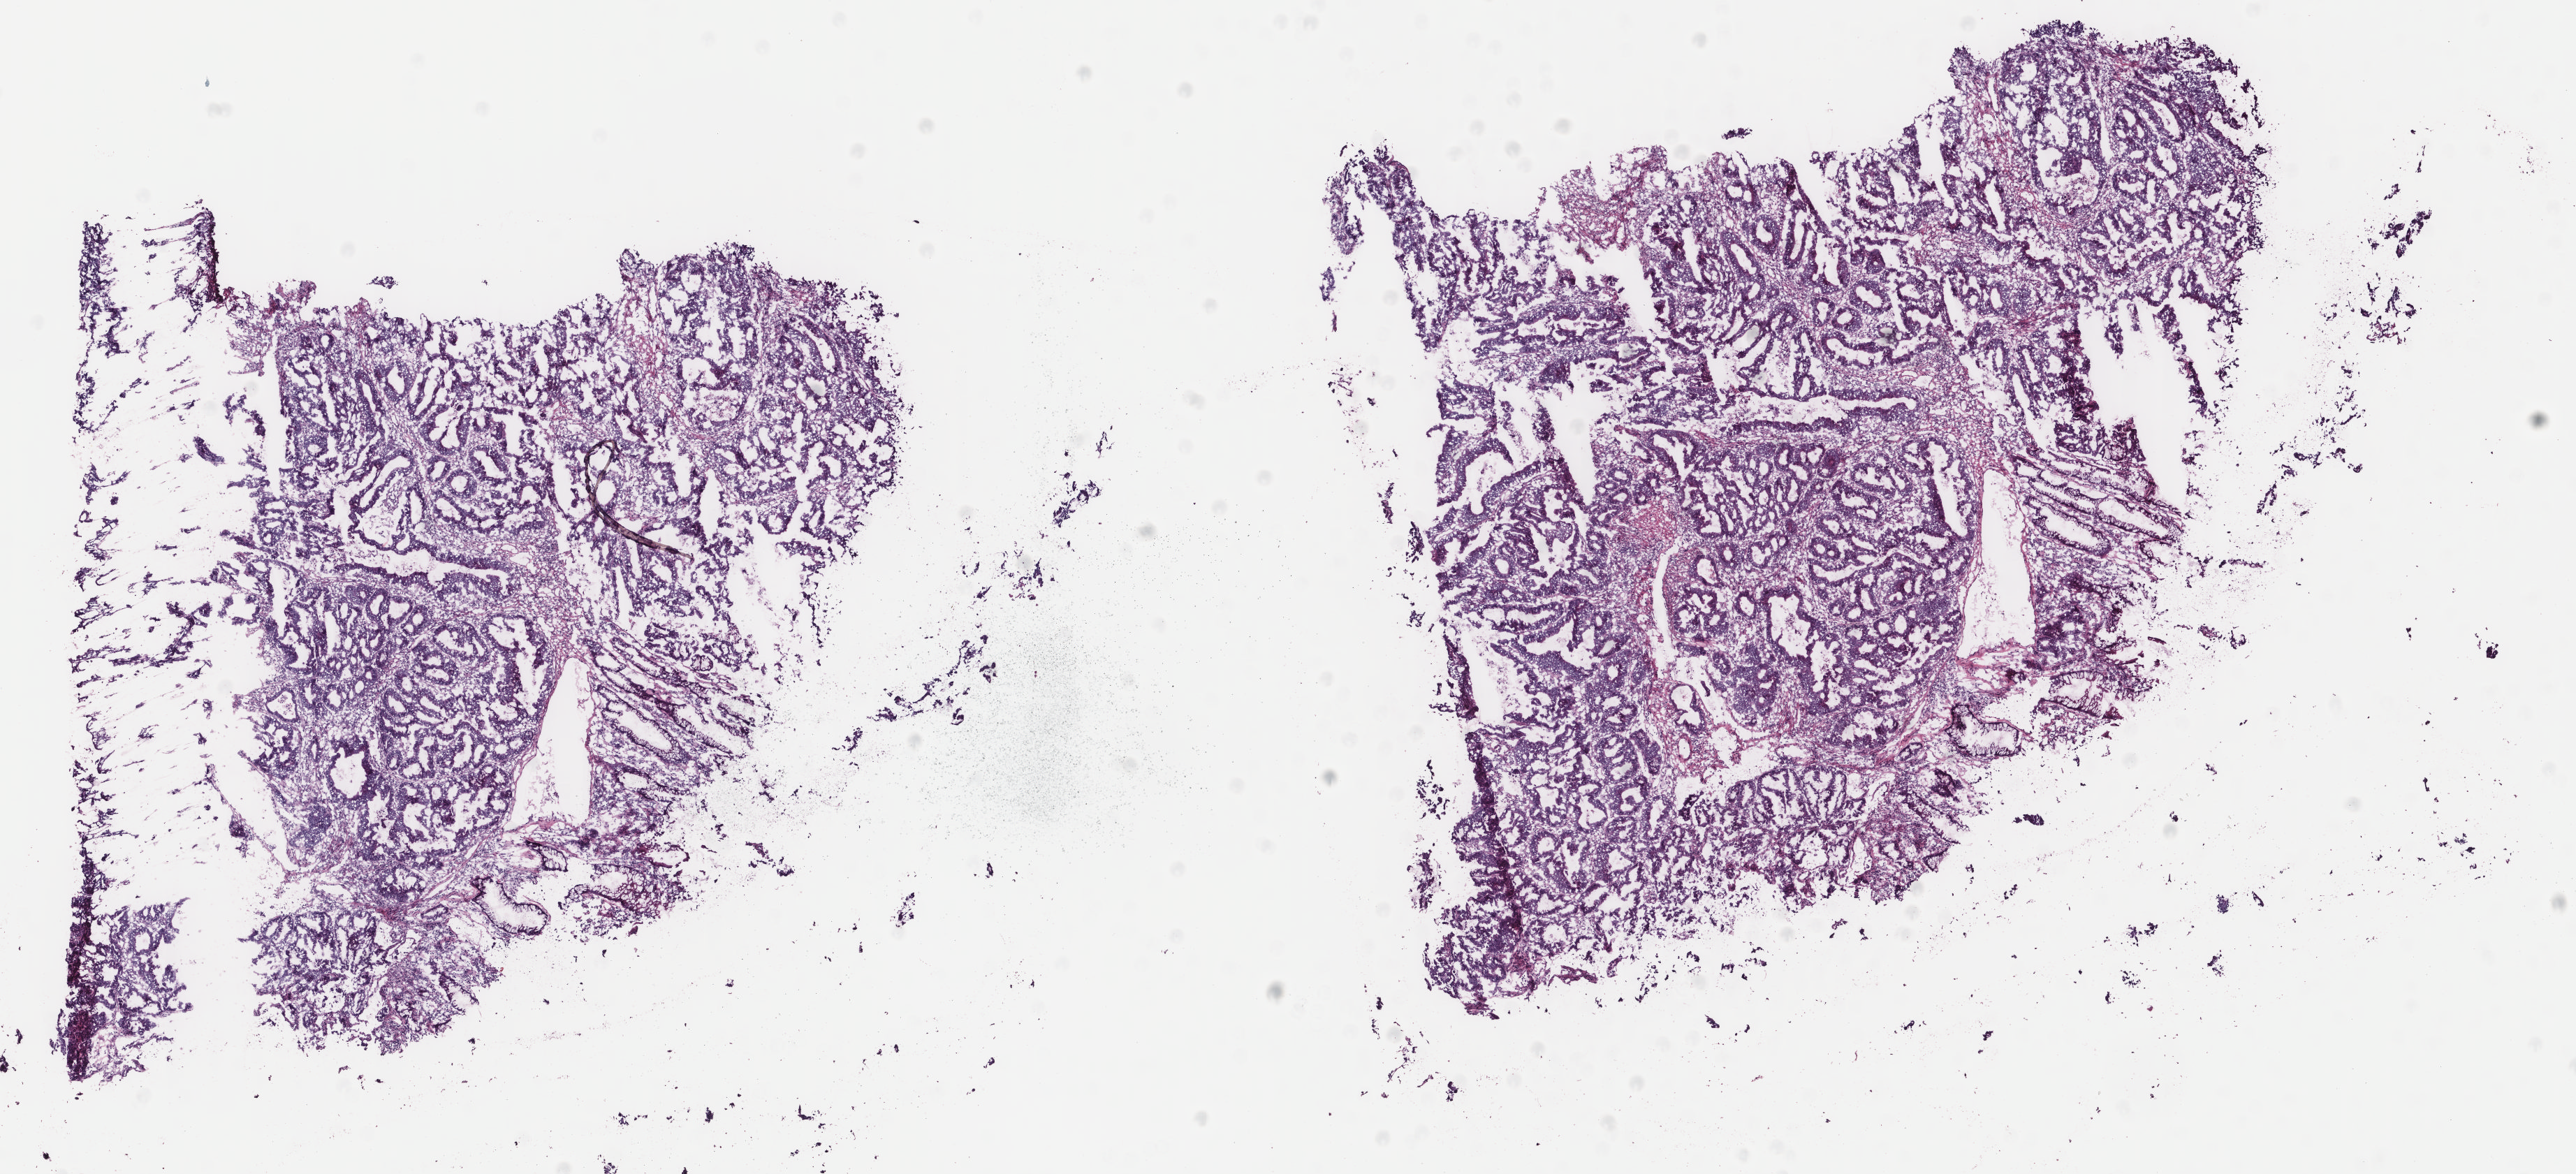
Digitized H&E tissue section (whole slide), whole scanned area (about 14.6 x 6.7 mm) shown as a low-resolution overview. Frozen section from the top of the tissue portion. Sample: primary tumour, colon. Female, age 71 years at initial diagnosis.
Diagnosis: Adenocarcinoma, NOS (ascending colon).